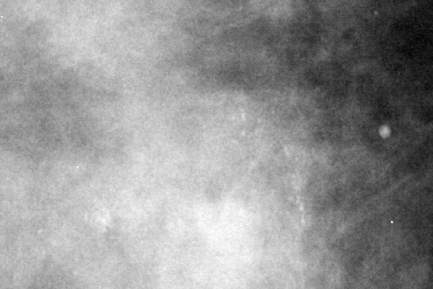
Crop from a digitized film mammogram around one marked abnormality; right breast; CC view.
- Finding: calcifications, morphology amorphous, distribution clustered; BI-RADS assessment category 4; subtlety rating 2 on a 1 (subtle) to 5 (obvious) scale; pathology (as recorded): benign.